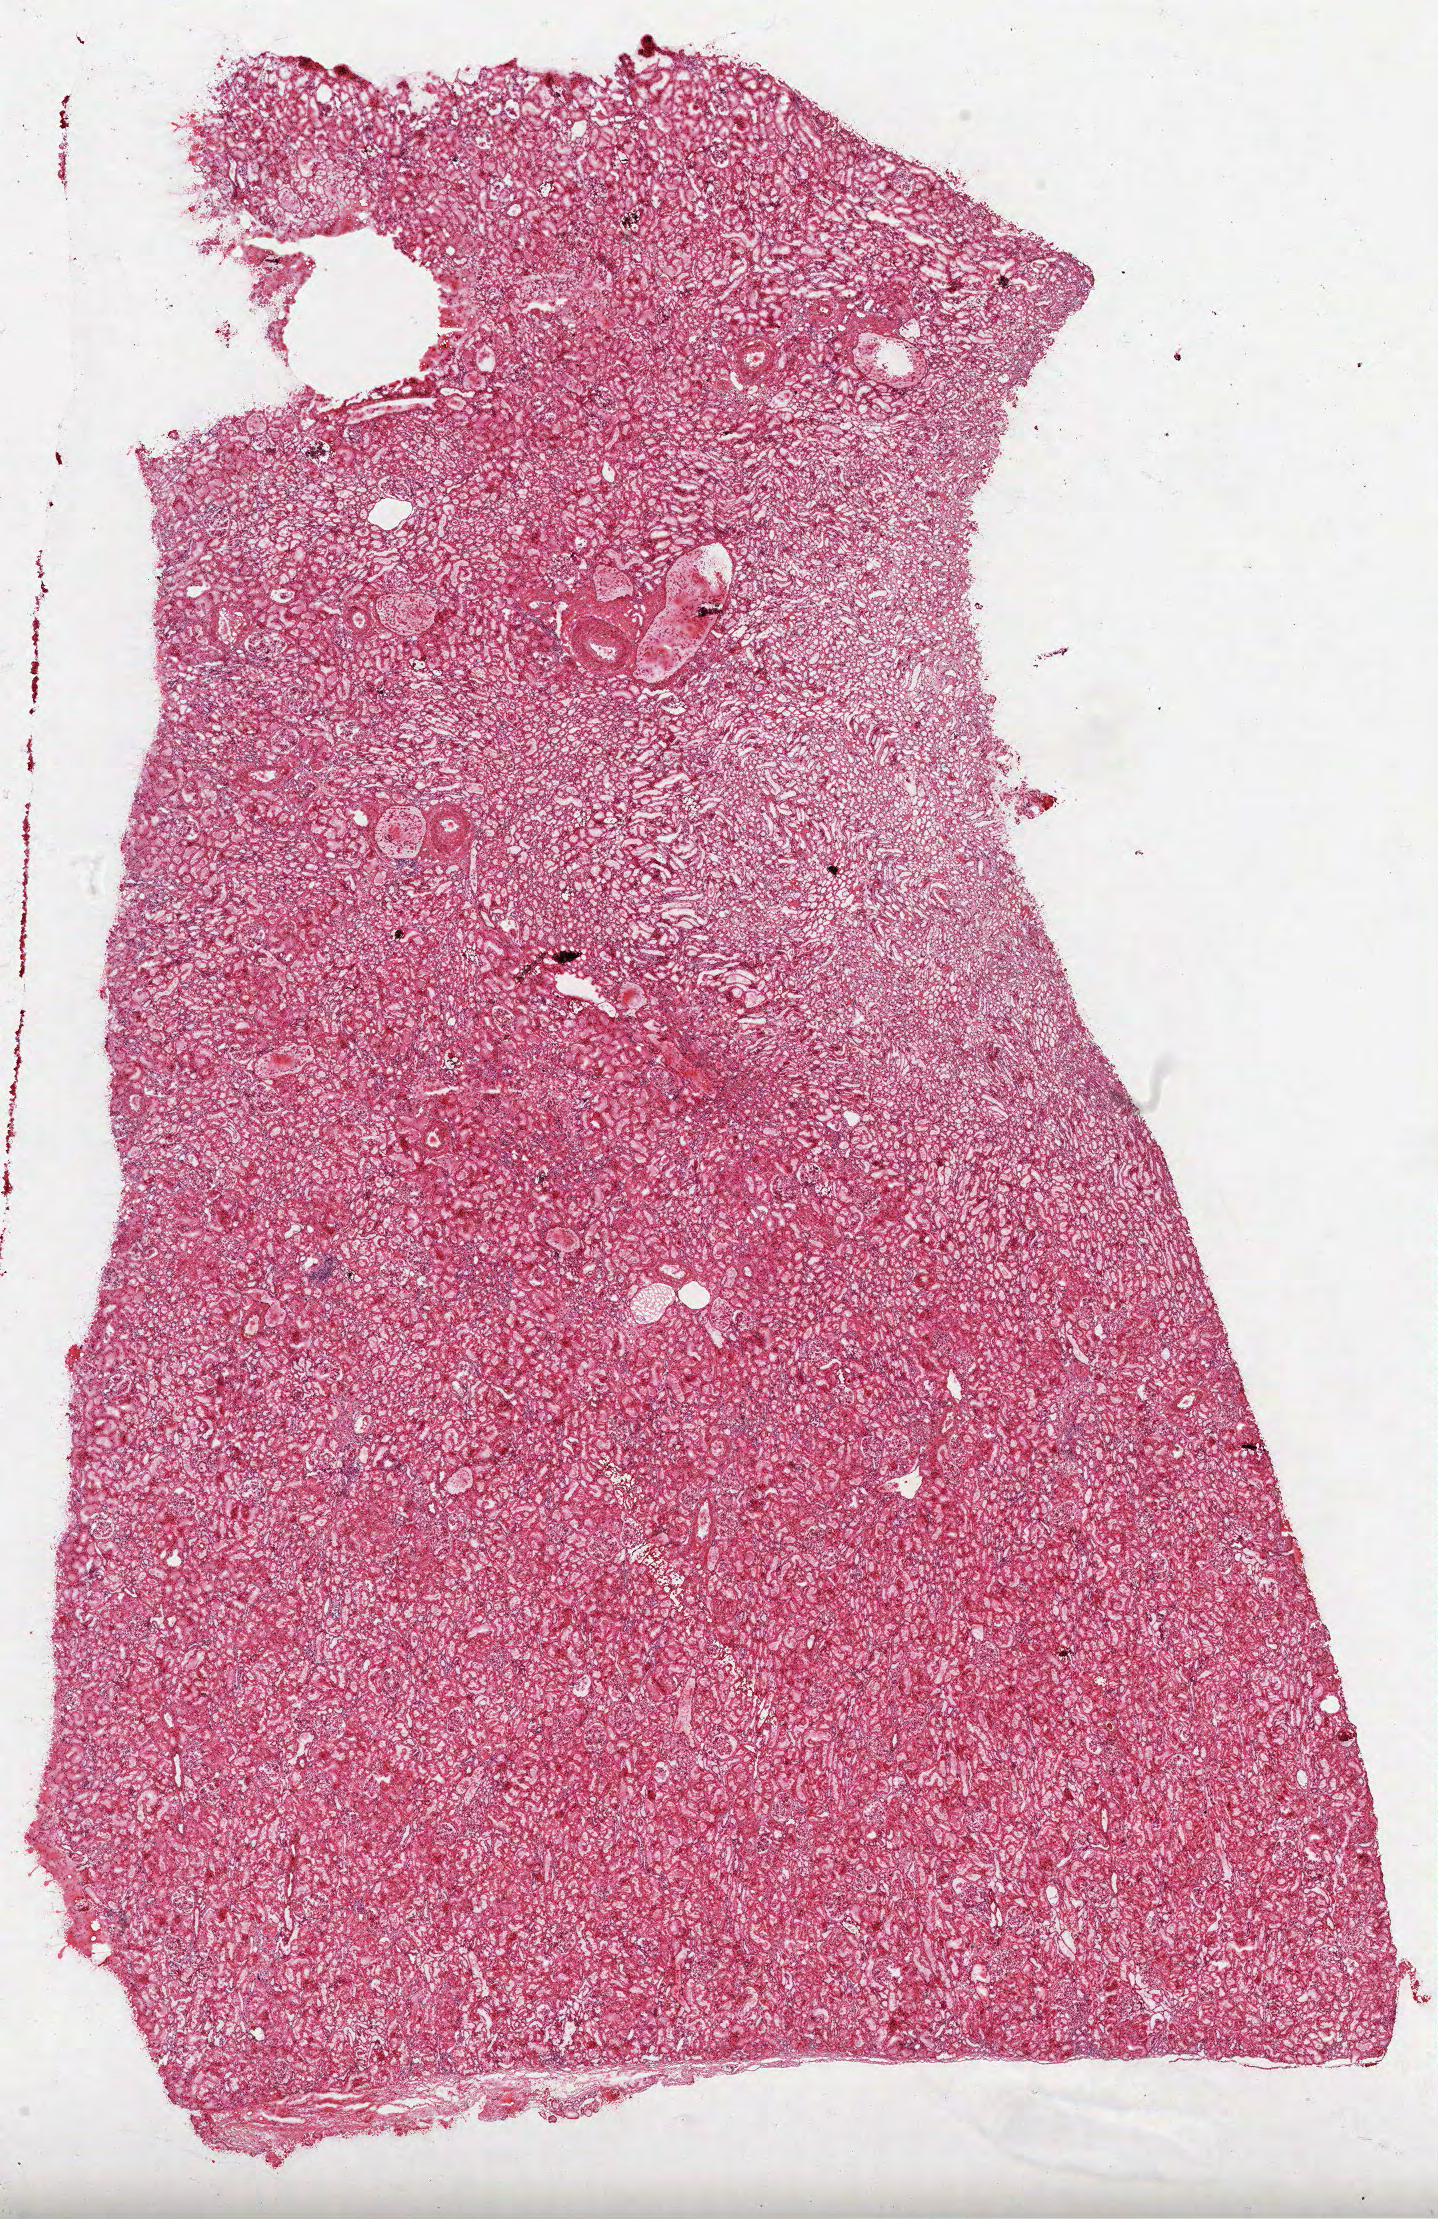
Whole-slide histology image, Hematoxylin and eosin (H&E) stained, whole scanned area (about 11.6 x 17.9 mm) shown as a low-resolution overview; frozen section from the top of the tissue portion; kidney, solid tissue normal (non-tumour tissue) sample. Patient: male, age at initial diagnosis 64 years.
This section: solid tissue normal (non-tumour) sample from the same patient. Patient diagnosis: Papillary adenocarcinoma, NOS.